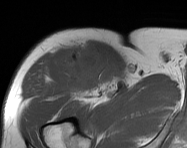
MRI of an extremity soft-tissue mass, one axial slice. Position 106 of 114 along the scan axis. MR volume resampled by the dataset authors to the PET/CT grid (not the native acquisition matrix). 3.27 mm slice thickness. 187 × 148 image matrix, field of view 183 × 145 mm. Male patient. From the clinical record (not read from this slice): histological type: pleiomorphic leiomyosarcoma; grade: intermediate; site of the primary tumour: right thigh.
Structures marked on this image (expert contour drawn on MRI and transferred to this co-registered scan by the dataset authors):
- gross tumour volume including surrounding oedema: bounding box <61,43,115,94> (left, top, right, bottom; pixels)
- gross tumour volume (mass): <68,52,112,92>